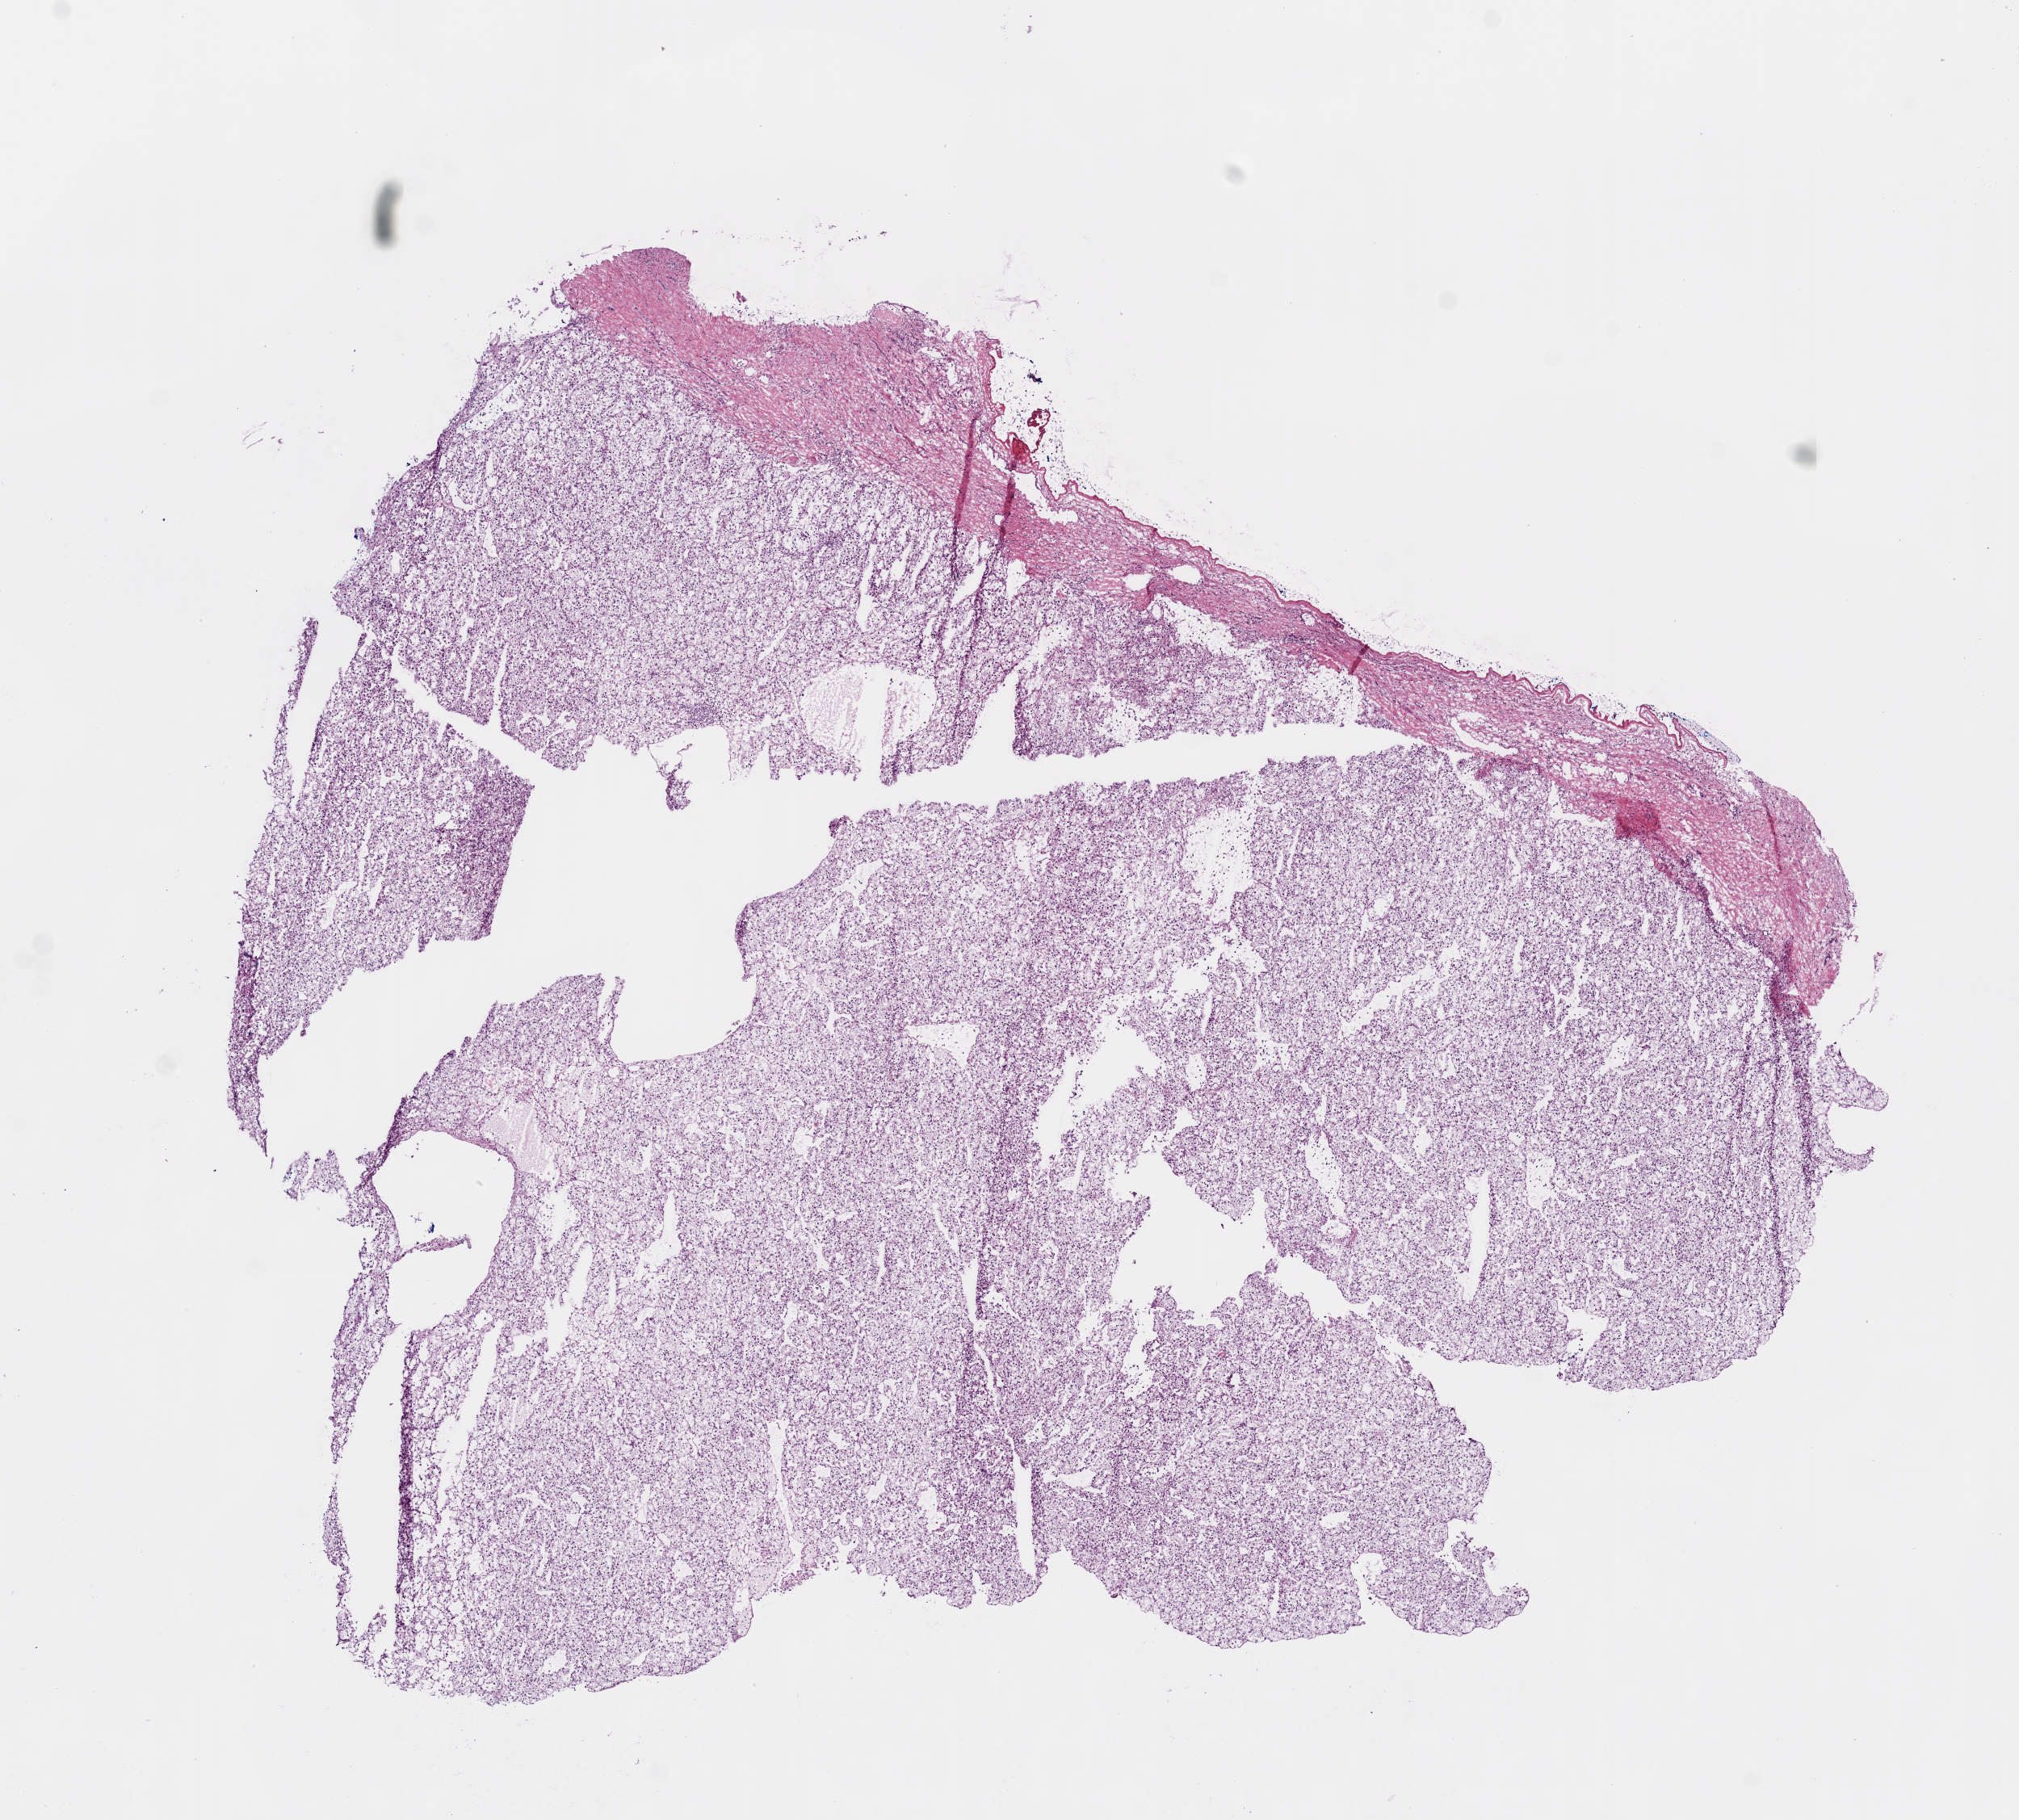
Digitized H&E-stained tissue section (whole slide) — low-resolution overview of the scanned area, about 10.0 x 9.0 mm (from a 20x scan); frozen section from the bottom of the tissue portion; primary tumour sample from the kidney. Female patient; age at initial diagnosis 55 years. Histologic grade: G2 (moderately differentiated). Composition of this section per pathologist review: tumour cells 90%, tumour nuclei 90%, stromal cells 10%, necrosis 0%. Inflammatory infiltration, as recorded: lymphocyte infiltration 5%.
Laterality: left. TNM: T1a NX M0. Diagnosis: Clear cell adenocarcinoma, NOS. AJCC pathologic stage: I.